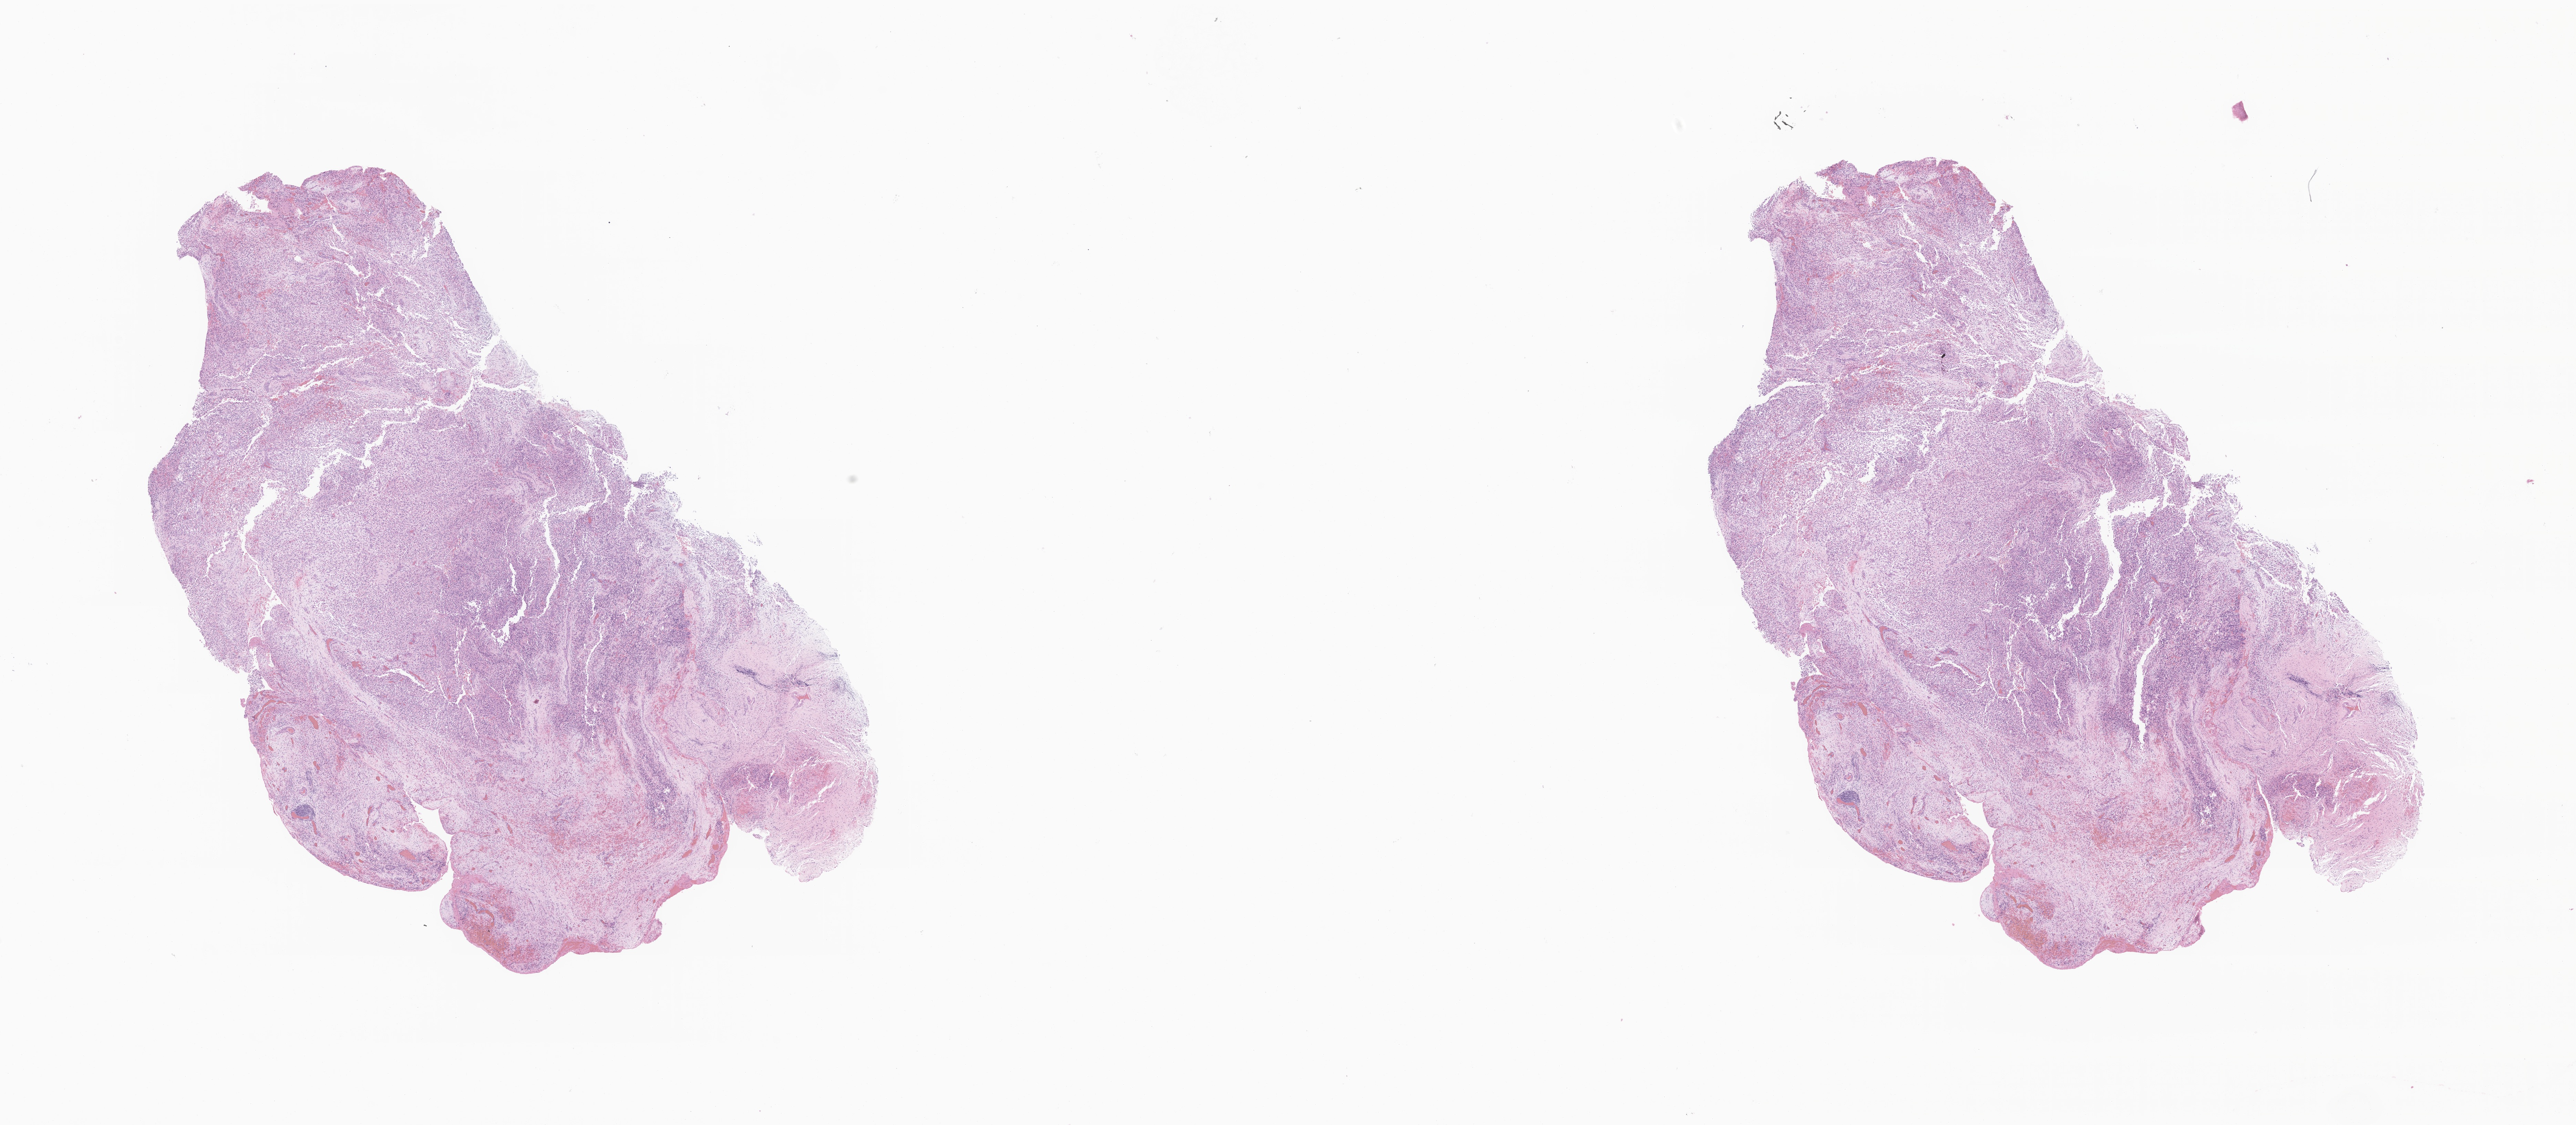
Hematoxylin and eosin (H&E) whole-slide image of tumor tissue from the orbit — shown as a low-resolution overview of the whole scanned area (about 31.5 x 13.8 mm); formalin-fixed paraffin-embedded section. Patient female; age 148 months (12 years 4 months).
Diagnosis (ICD-O-3 morphology term): Neoplasm, uncertain whether benign or malignant.